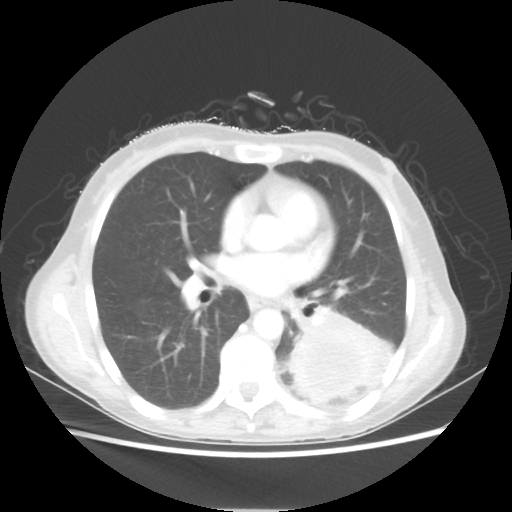
Chest CT, one axial slice; slice 28 of 56 in the series (ordered by position); lung window (W 1500 / L -600 HU); 512 × 512 image matrix, field of view 360 × 360 mm. Patient: female, 53 years. From the clinical record (not read from this slice): clinical TNM (as recorded): T3 N0 M0.
Structures marked on this image (rectangle marked by the reading radiologist):
- lung tumour (recorded histology: adenocarcinoma): box from (x=285, y=305) to (x=394, y=404) px